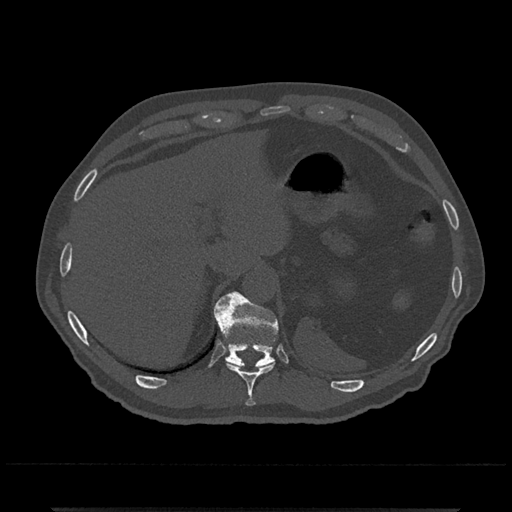
CT including the spine, one axial slice; slice 526 of 797 in the series (ordered by position); reconstruction kernel Br40s/3; bone window (W 1800 / L 400 HU); 0.5 mm slice thickness; 512 × 512 image matrix, field of view 393 × 393 mm. Male patient, age 67 years. Case-level facts recorded for this patient, not image findings: primary cancer: prostate.
Outlined on this slice (semi-automatic segmentation, software-assisted and operator-edited):
- T10 vertebra: box from (x=219, y=325) to (x=275, y=407) px
- T11 vertebra: (x=214, y=292)–(x=278, y=368)